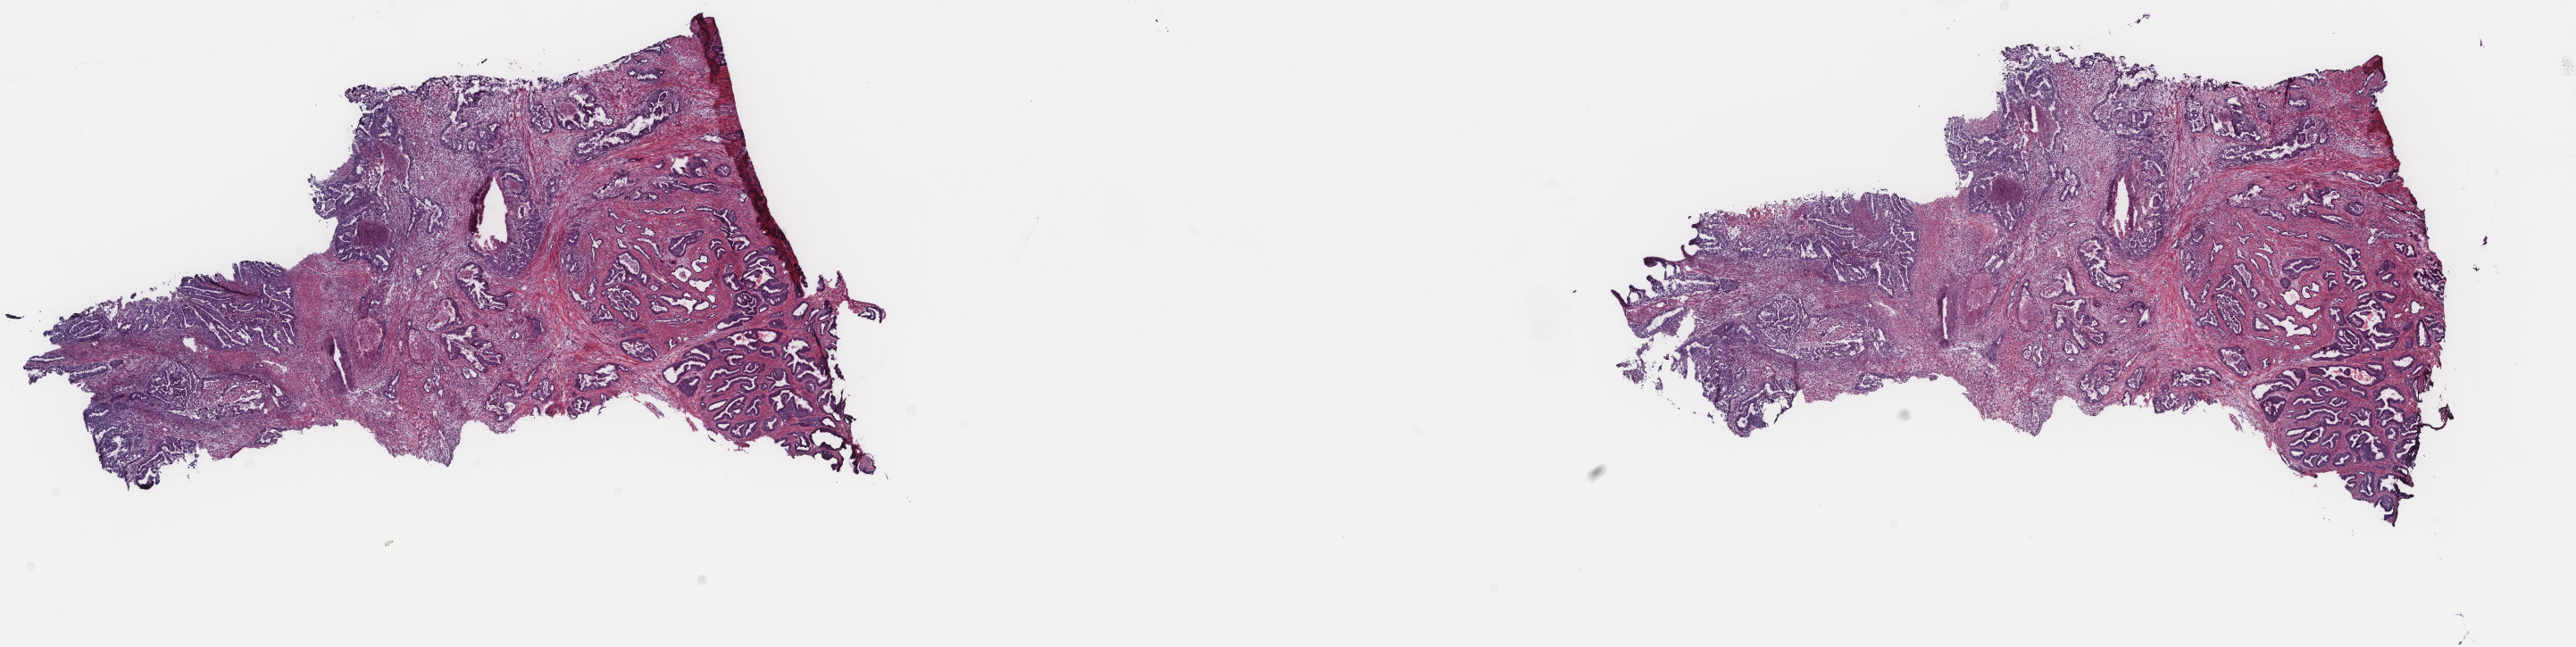
Digitized H&E-stained tissue section (whole slide), whole scanned area (about 22.9 x 5.8 mm) shown as a low-resolution overview, frozen section from the top of the tissue portion, primary tumour sample from the uterus. Female patient; age at initial diagnosis 75 years.
Diagnosis: Endometrioid adenocarcinoma, NOS (endometrium).